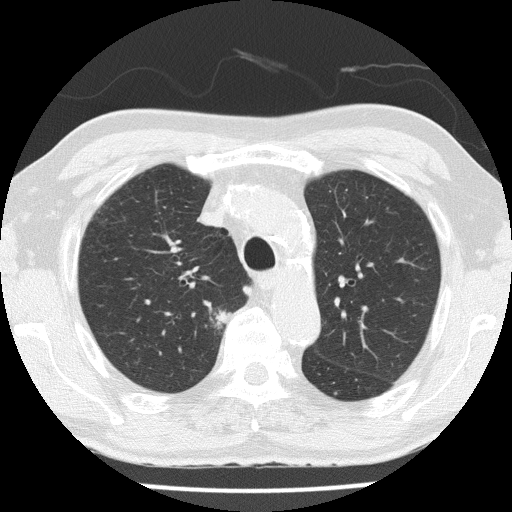
Low-dose screening chest CT, one axial slice; slice 109 of 153 in the series (ordered by position); 120 kVp; lung window (W 1500 / L -600 HU); 2 mm slice thickness; 512 × 512 image matrix.
Outlined on this slice (expert manual segmentation):
- lesion 1 (tumor, upper lobe of right lung): bounding box [x1, y1, x2, y2] px = [211, 311, 234, 325]